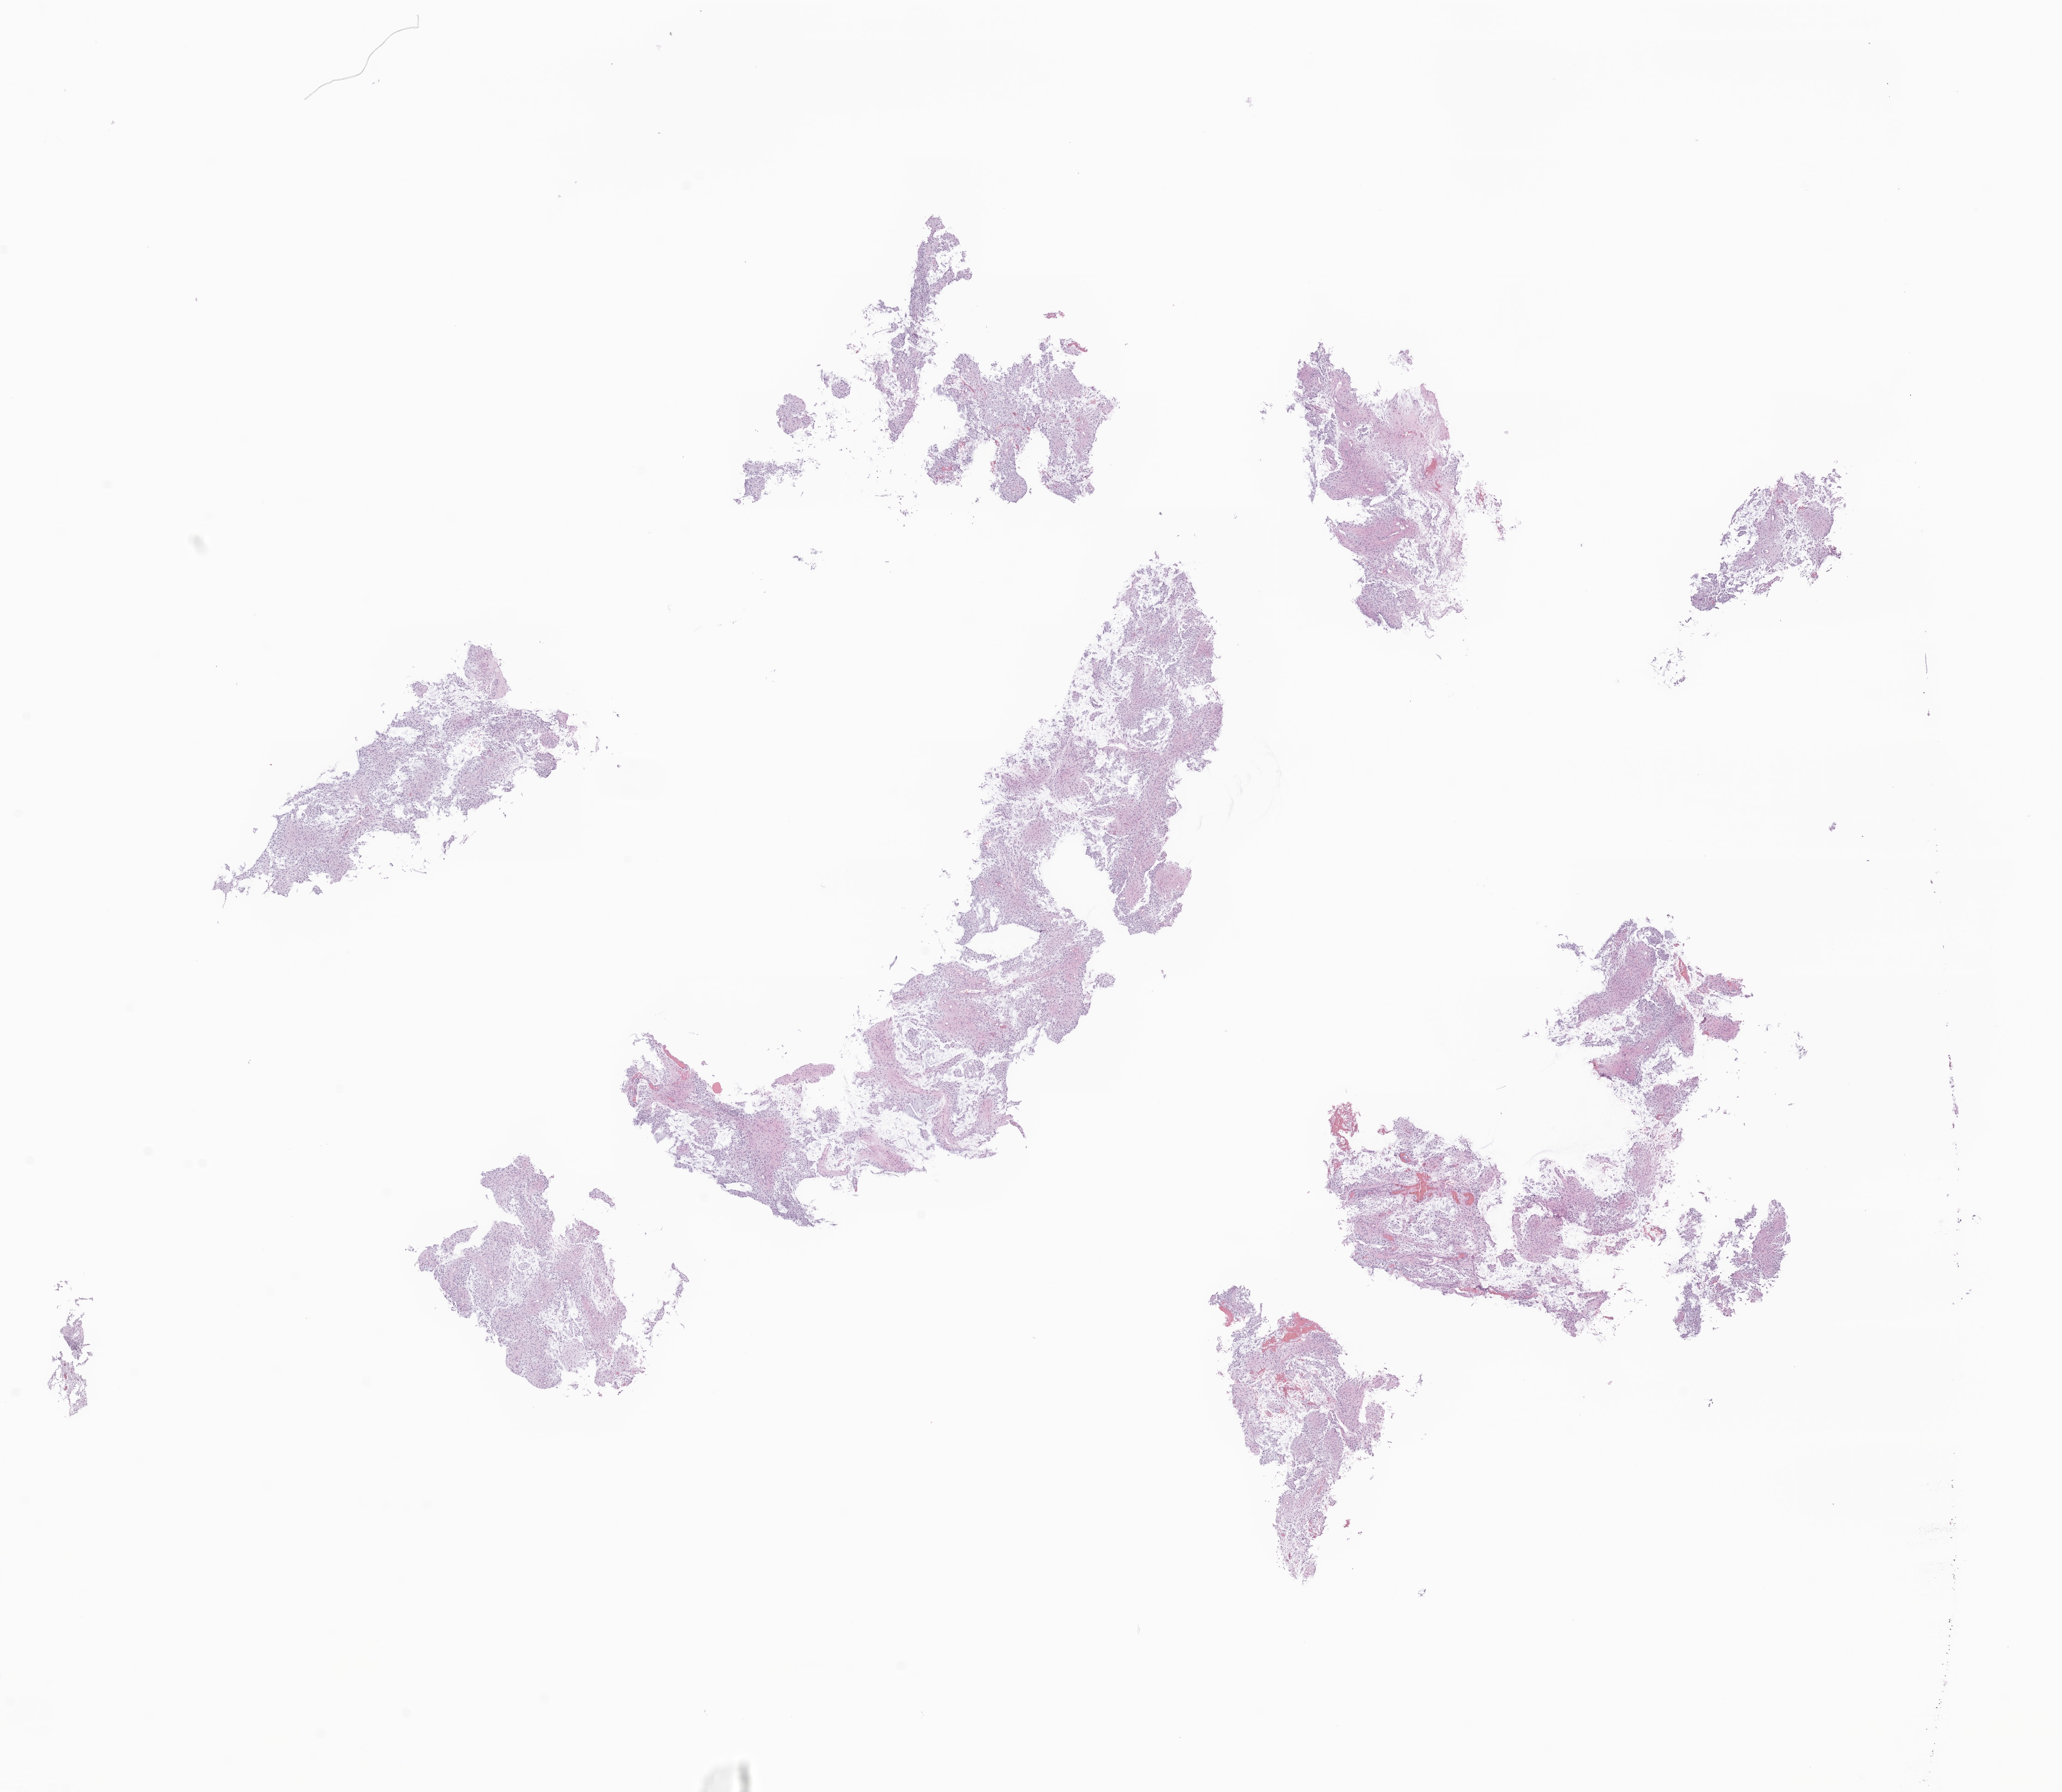
Hematoxylin and eosin (H&E) whole-slide image of tumor tissue from the brain stem, whole scanned area (about 18.8 x 16.4 mm) shown as a low-resolution overview; formalin-fixed paraffin-embedded section. Patient female; age 164 months (13 years 8 months).
Diagnosis (ICD-O-3 morphology term): Pilocytic astrocytoma.